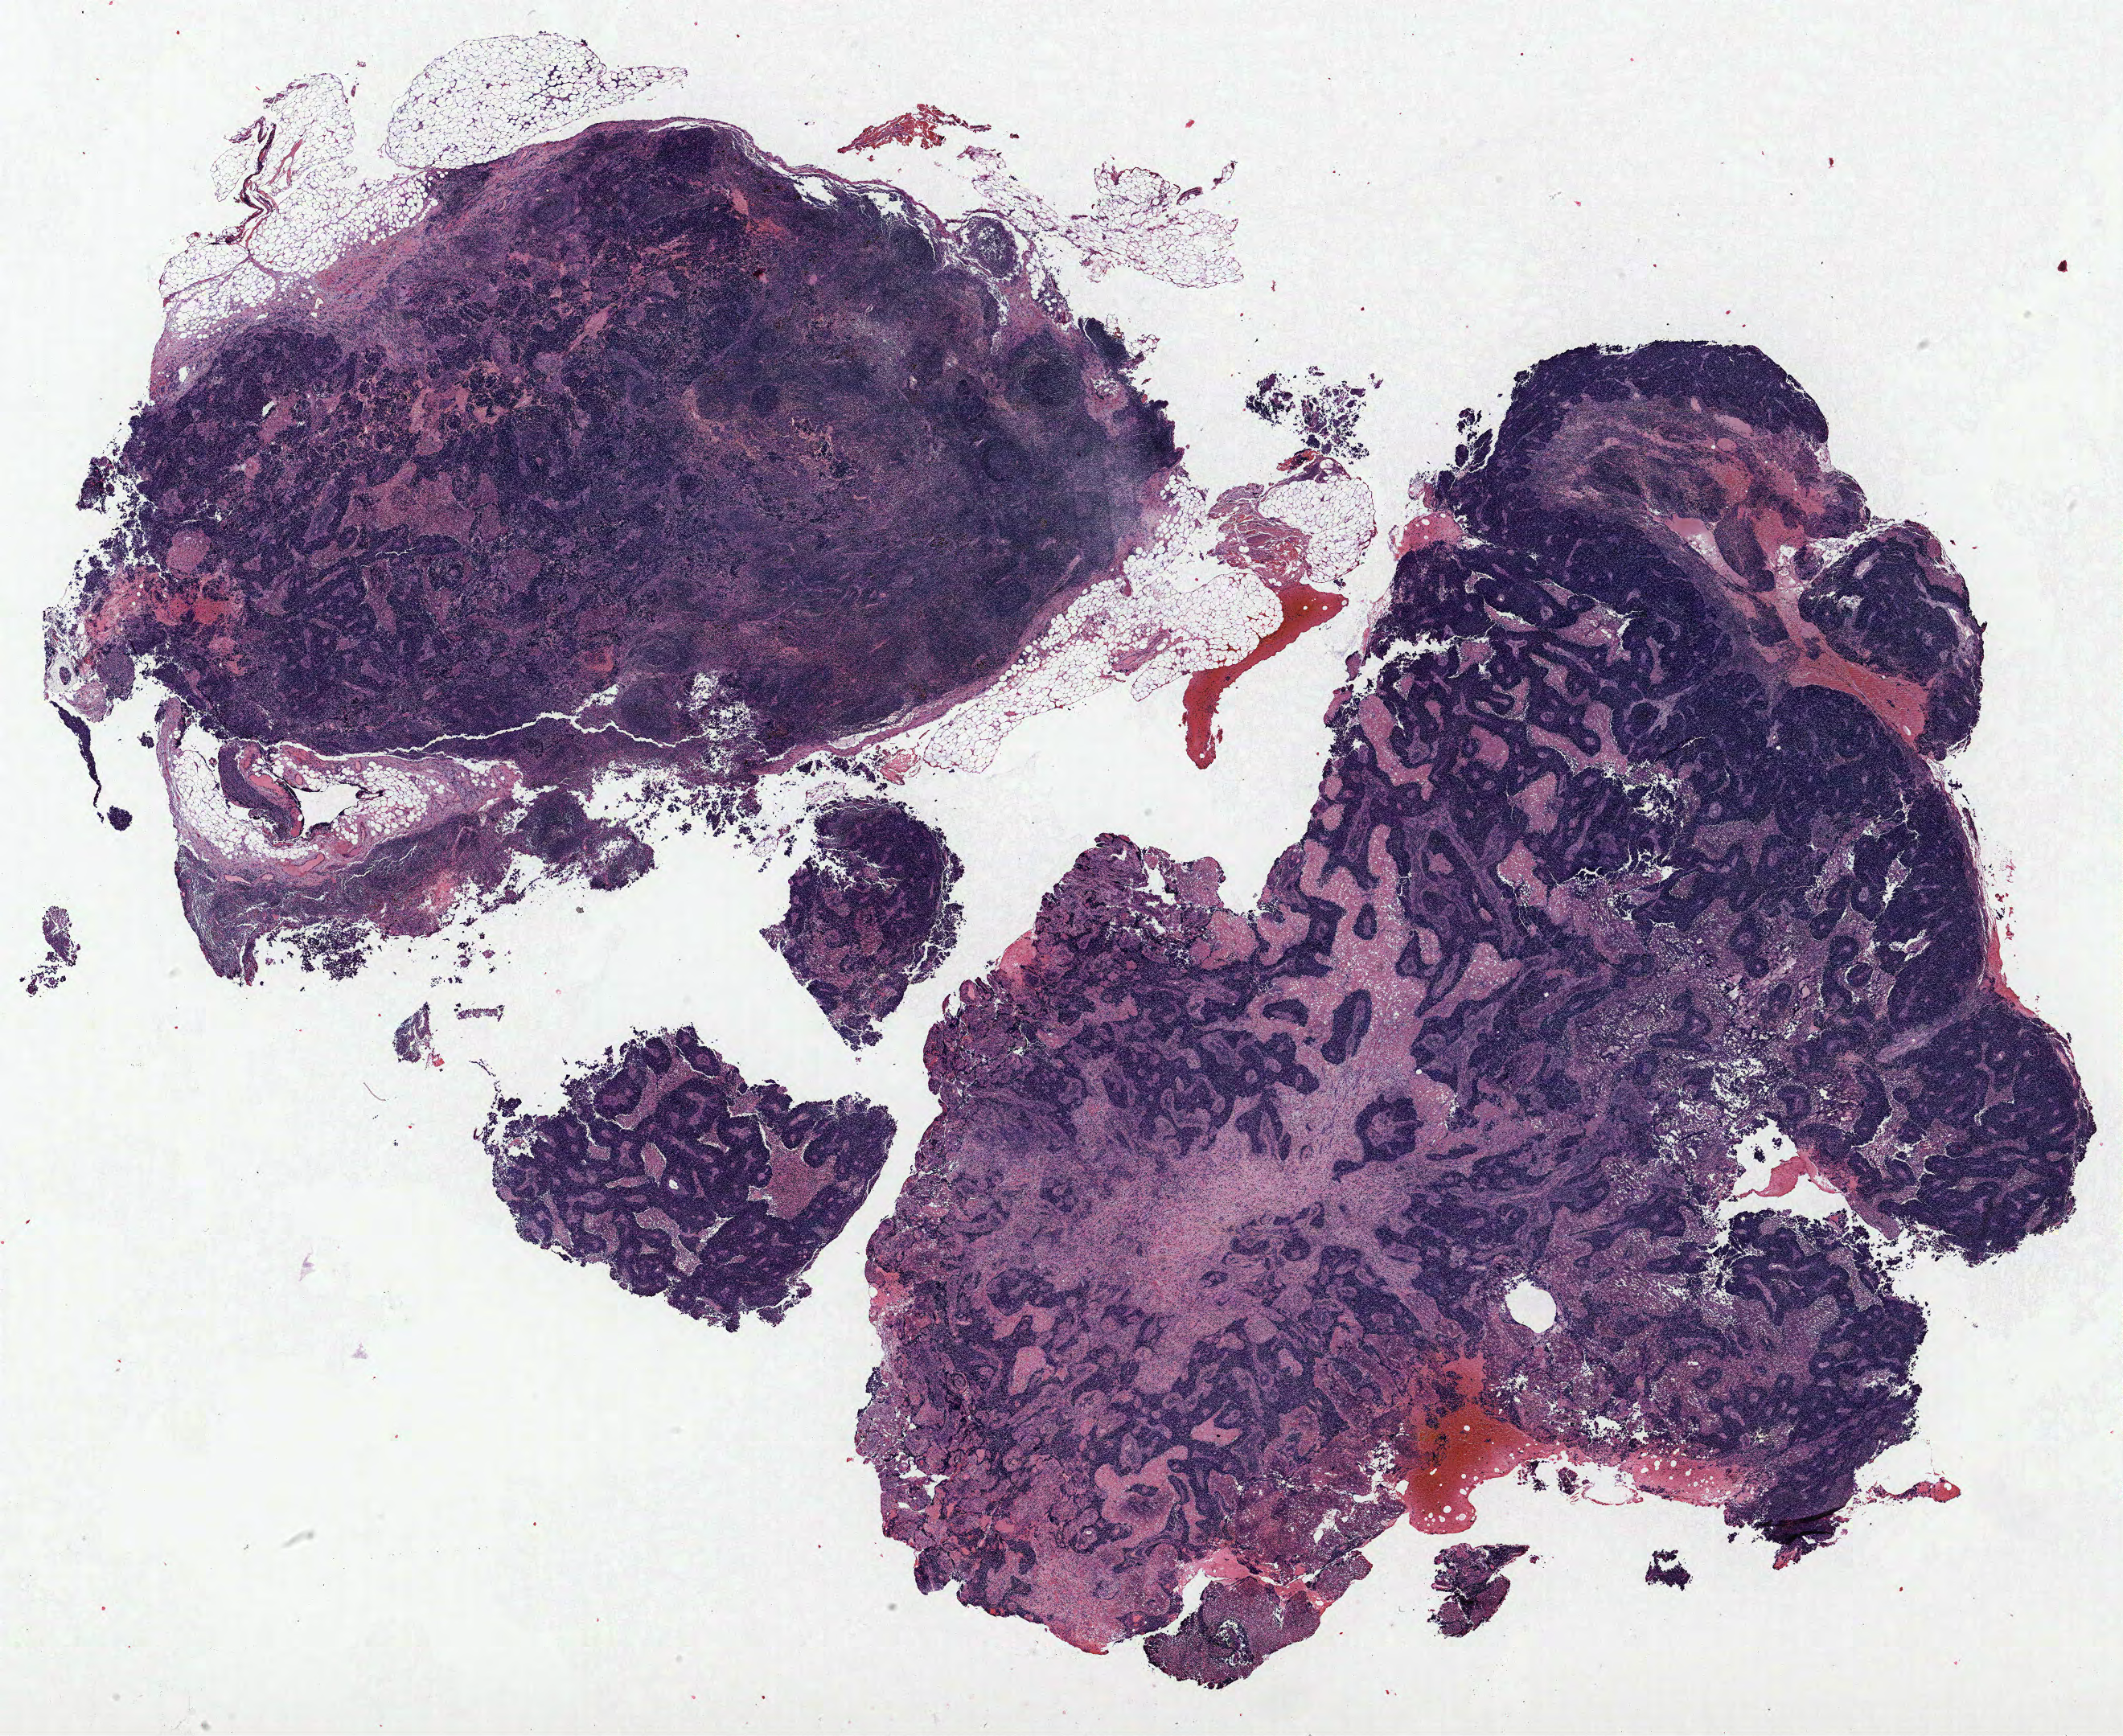
Hematoxylin and eosin (H&E) stained whole-slide image, shown as a low-resolution overview of the whole scanned area (about 21.1 x 17.3 mm, slide scanned at 40x); FFPE section; lung tissue. Male, age 56 at enrolment. Current smoker at enrolment.
- tumour size (pathology): 10 mm
- stage (AJCC 6th edition): IIIA
- primary tumour location (clinical record): right upper lobe
- ICD-O-3 topography: upper lobe of lung (C34.1)
- participant's lung-cancer diagnosis: Large cell neuroendocrine carcinoma